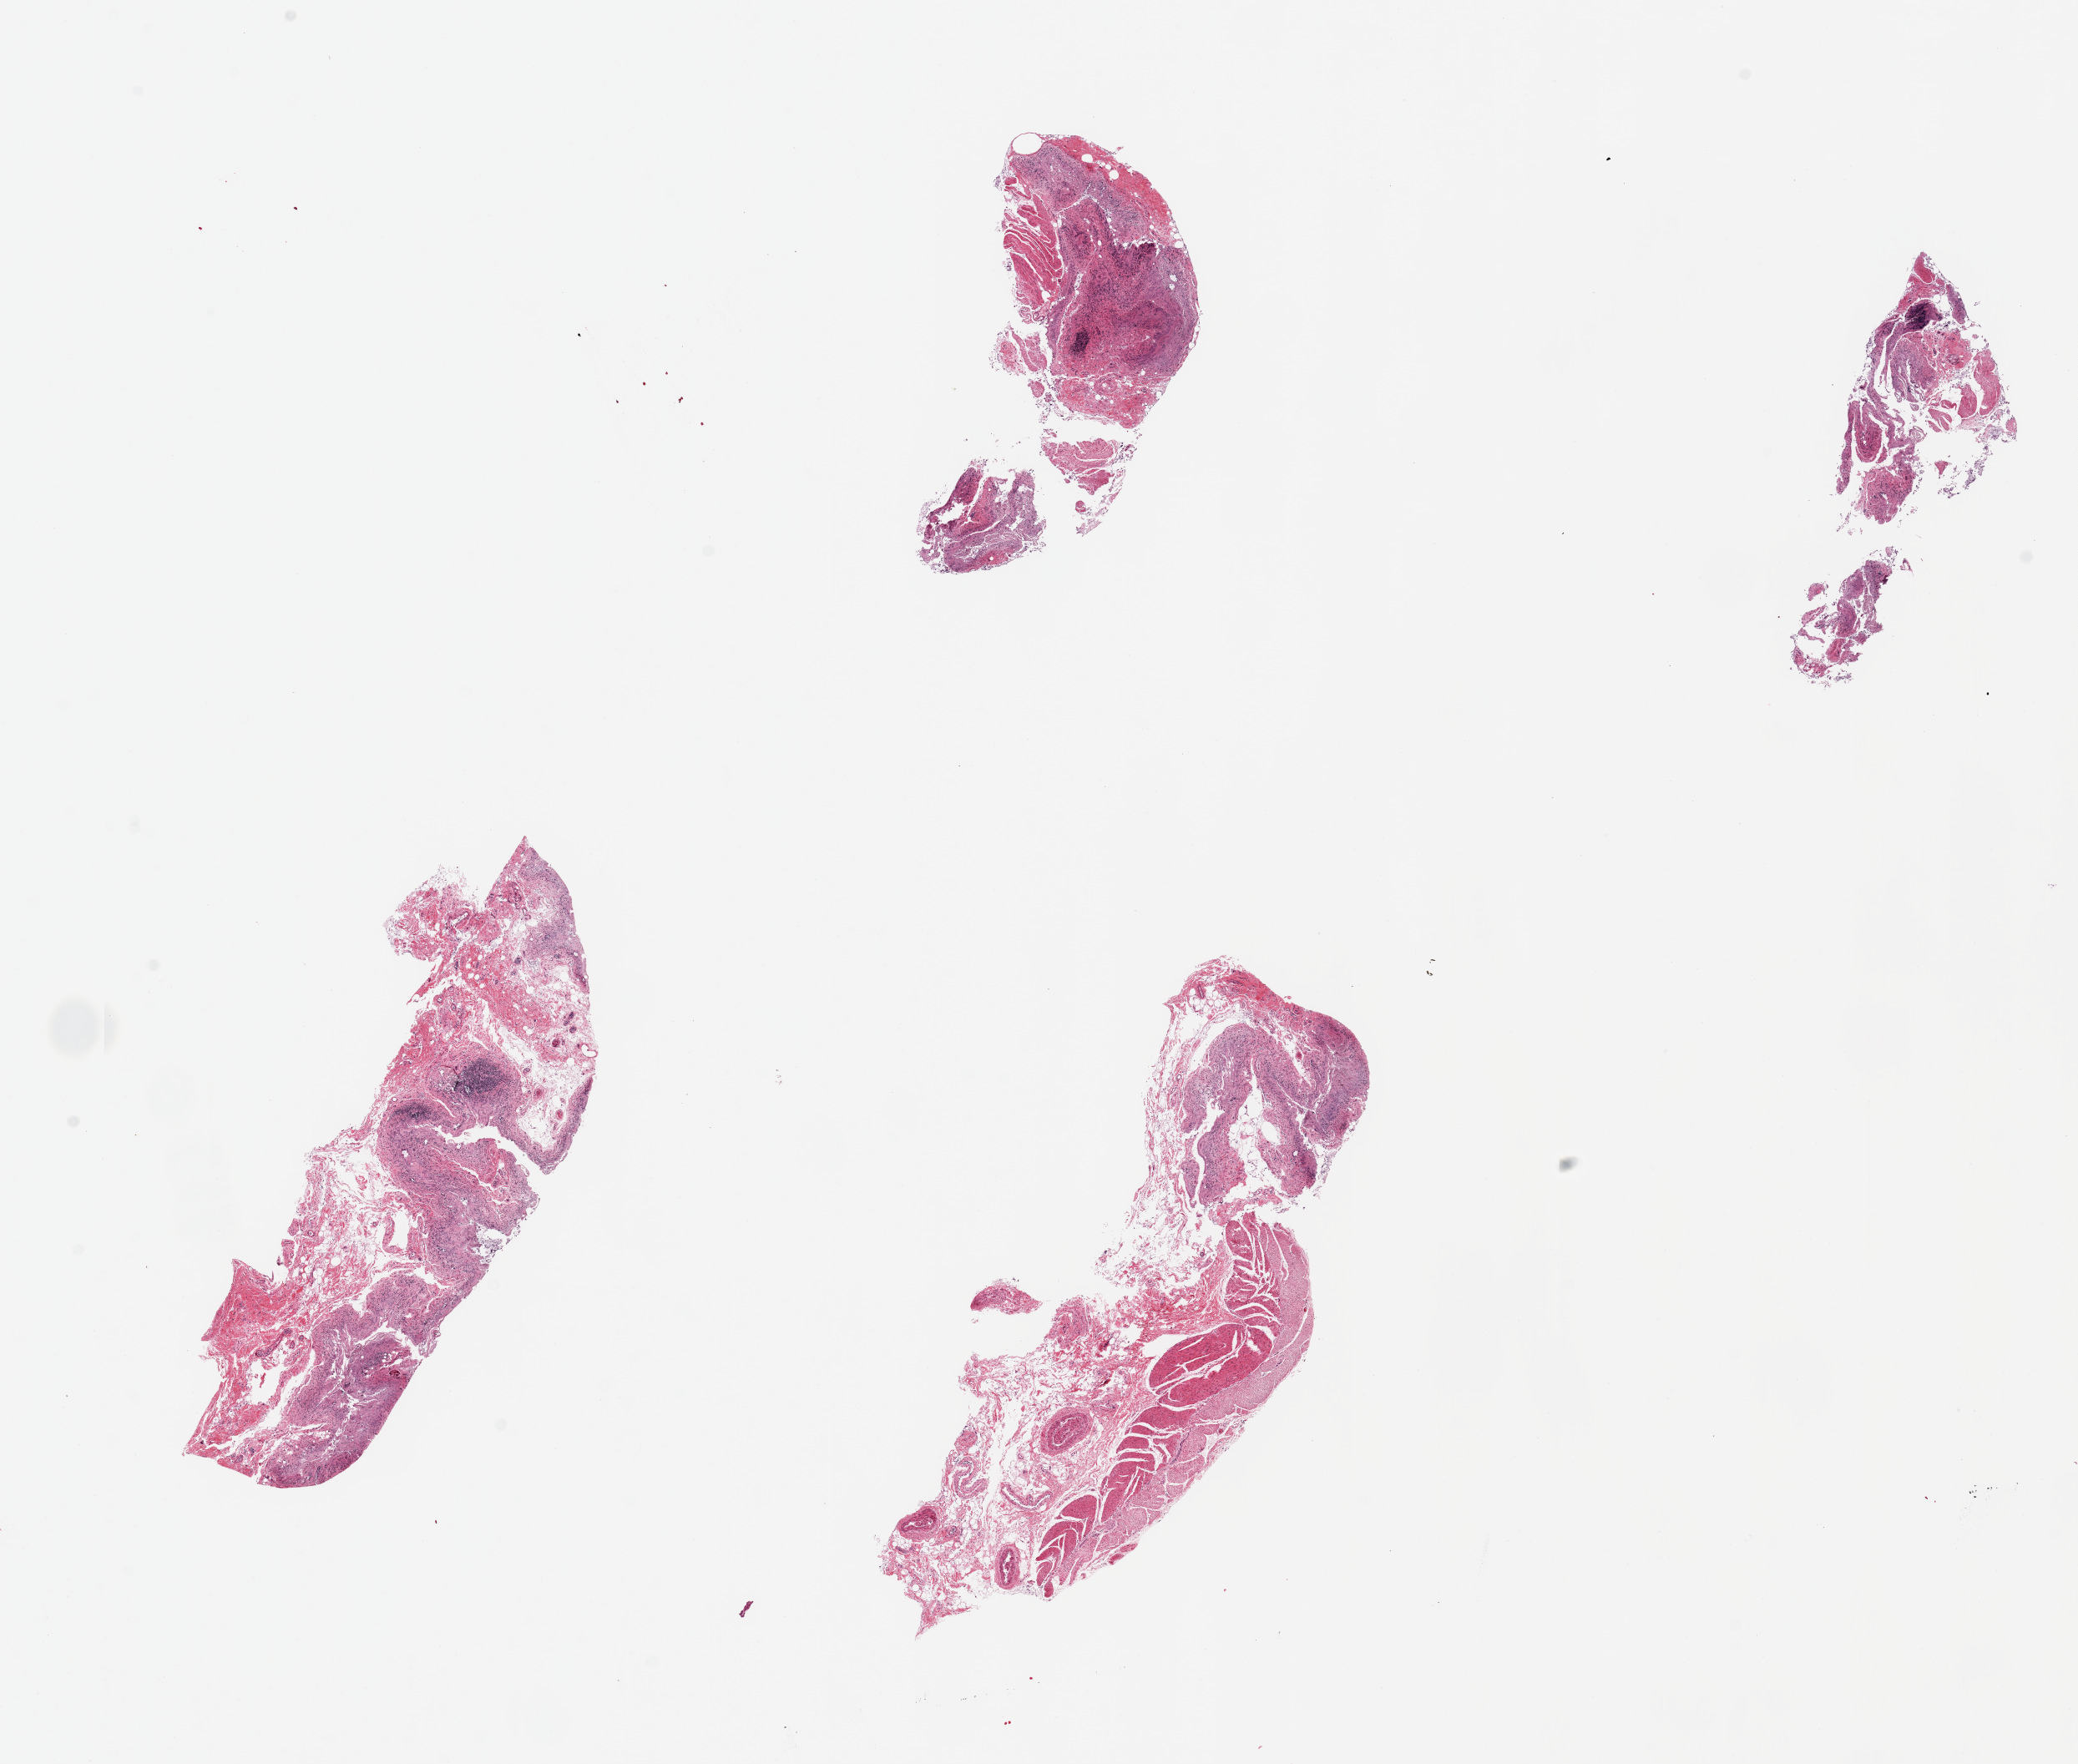
Digitized H&E-stained section, low-resolution overview of the scanned area, about 19.7 x 16.7 mm (from a 20x scan), PAXgene-fixed paraffin-embedded (PFPE) section, target tissue: ileum, tissue donor sample.
Review note (as recorded): 4 pieces, up to 7x3mm; mostly mucosa/submucosa (targets) but extensively autolyzed; small lymphoid foci.